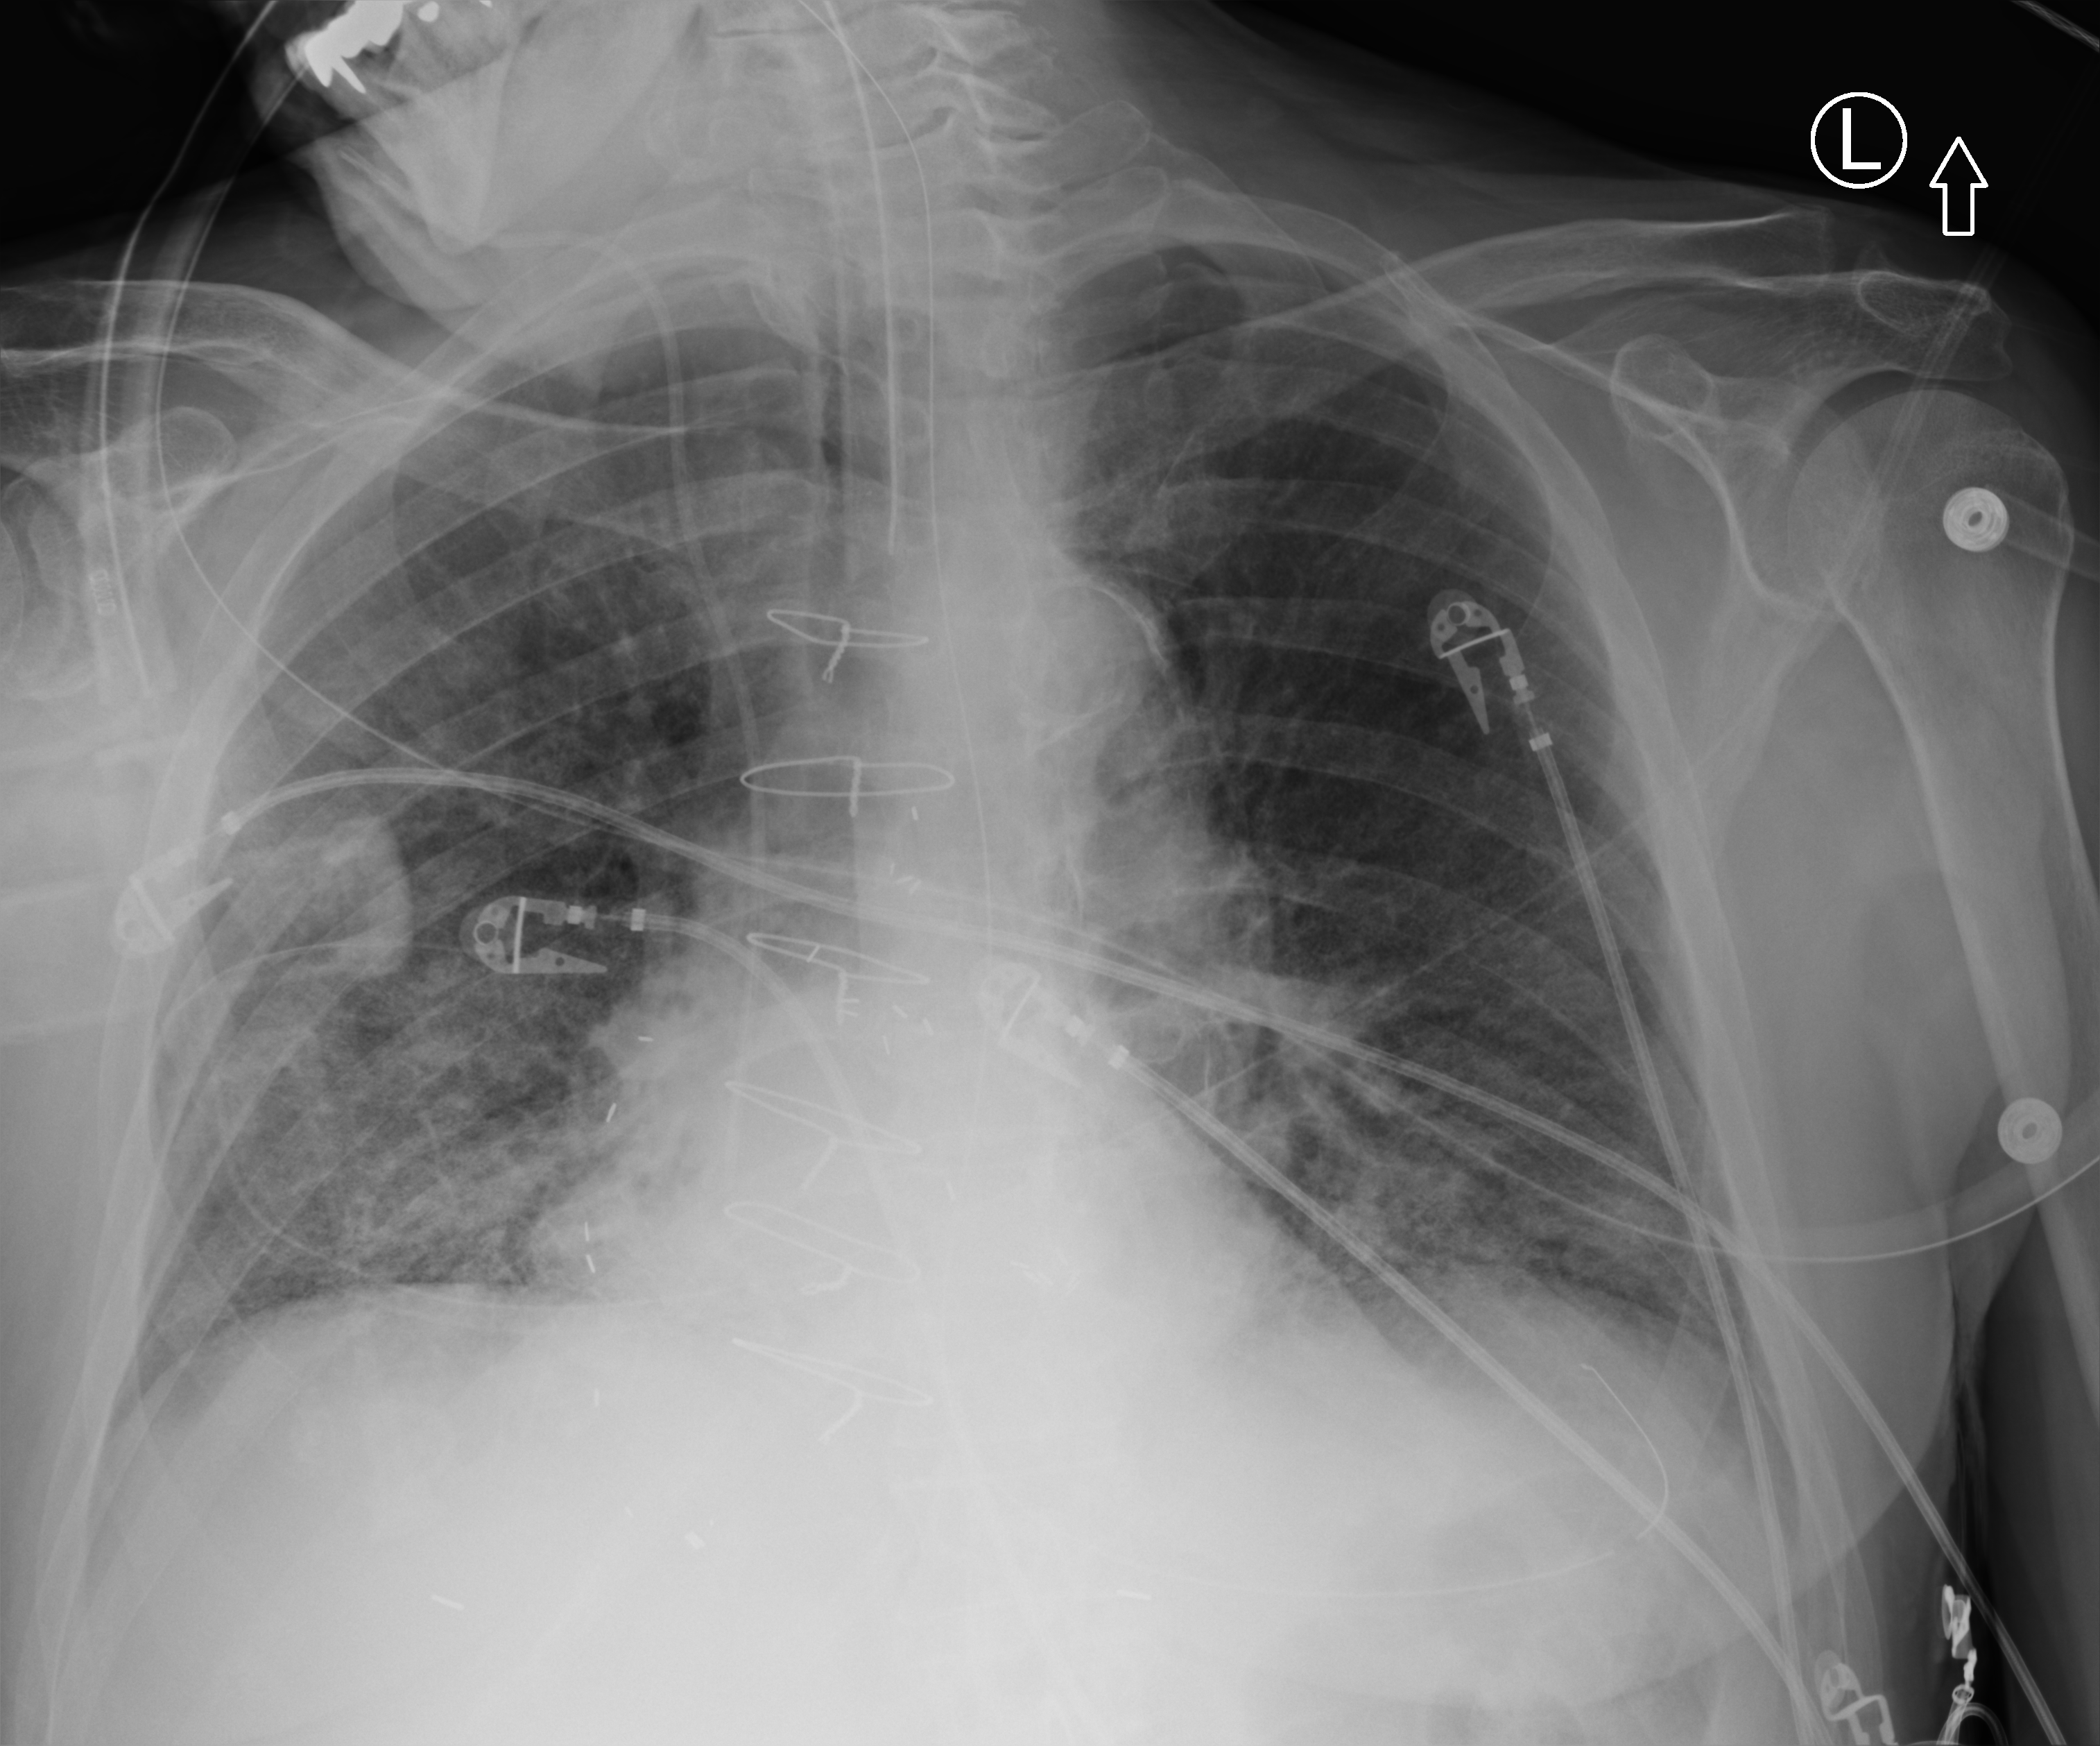
Bedside chest radiograph (computed radiography); anteroposterior (AP) projection. Male patient hospitalised with COVID-19, age 75–90 years.
Admission-level facts for this patient (not findings on this image; timing relative to this image not recorded): admitted to intensive care during this hospital stay: yes; mechanically ventilated during this hospital stay: yes; COPD (admission record): no.